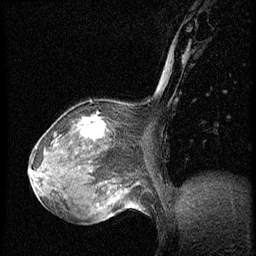
Breast MRI (dynamic contrast-enhanced), one sagittal slice; position 24 of 56 along the scan axis; dynamic contrast-enhanced series, image 2 of 3 at this slice position (ordered by acquisition); 1.5 T; TE 4.2 ms, TR 20.4 ms; 2 mm slice thickness; 256 × 256 image matrix, field of view 200 × 200 mm. Female patient, age 64 years. Case-level facts recorded for this patient, not image findings: setting: breast cancer imaged before/during neoadjuvant chemotherapy; receptor status: HR-positive, HER2-negative.
Outlined on this slice (semi-automatically segmented with operator editing):
- analysis volume of interest (the breast-tissue region the enhancement analysis was run in; not a lesion): bounding box [x1, y1, x2, y2] px = [48, 101, 140, 186]
- tumour enhancement mask (voxels above the 70 % enhancement threshold inside the analysis volume of interest): [78, 115, 105, 140]